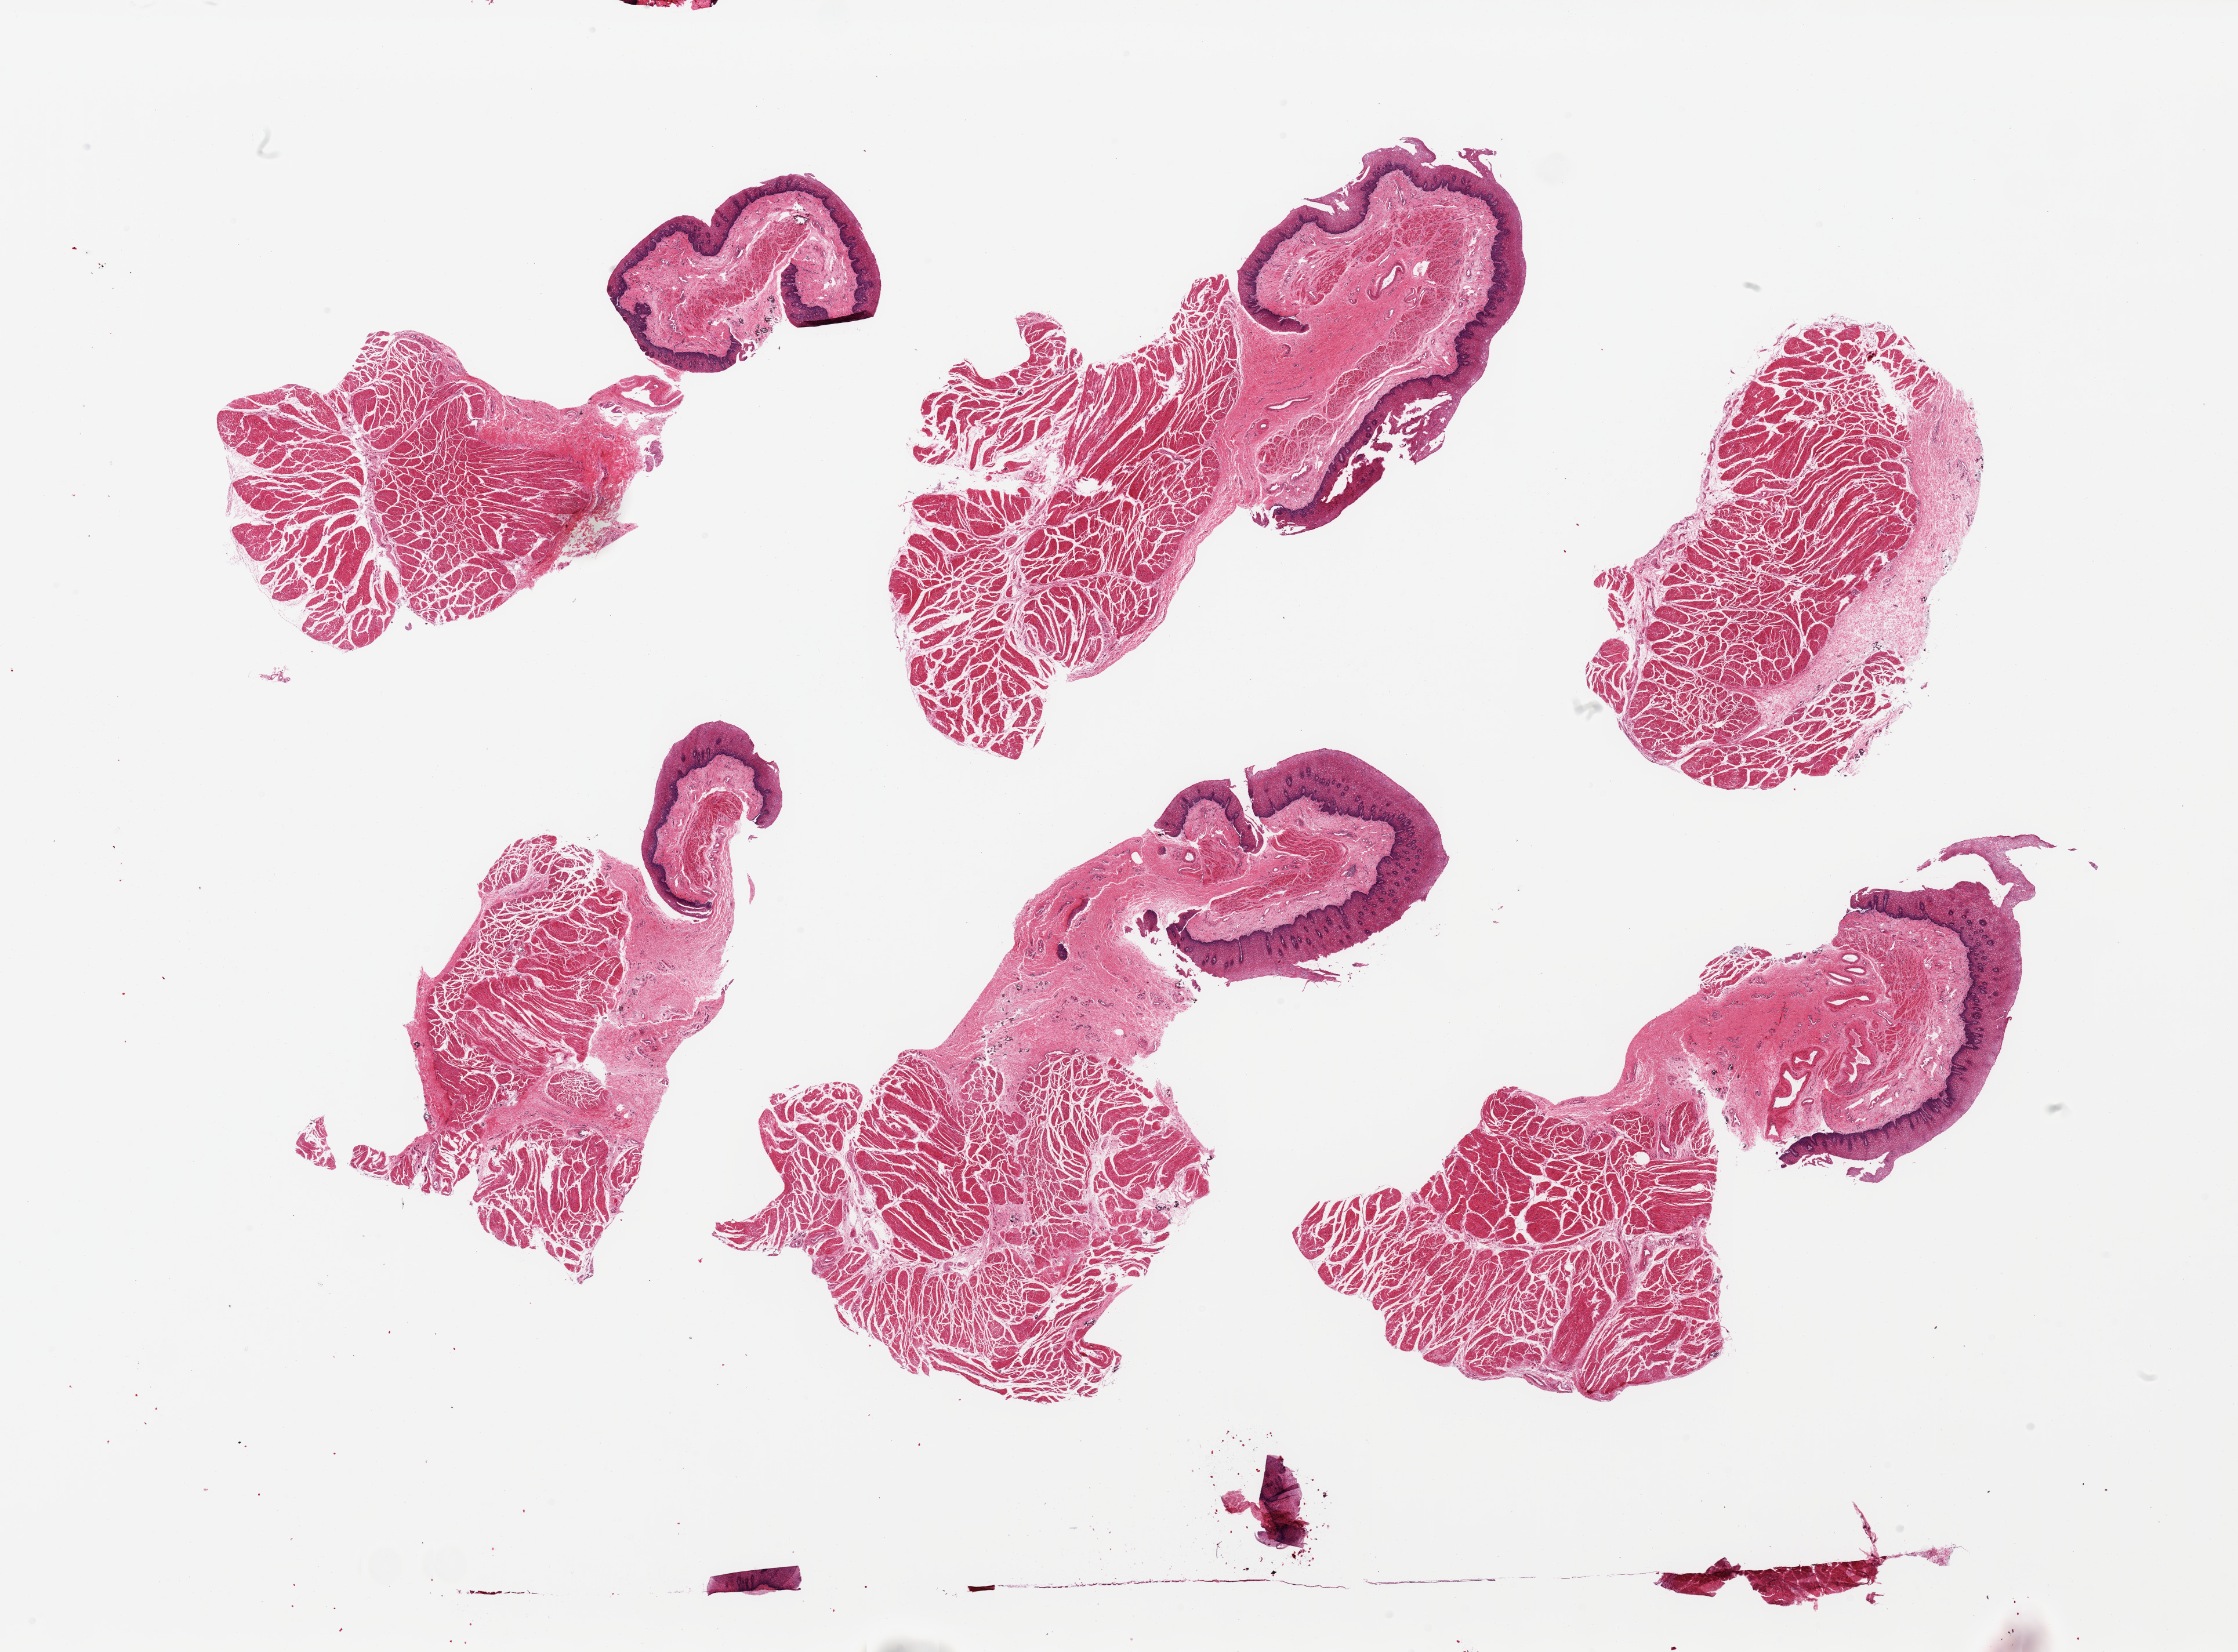
Whole-slide image, haematoxylin and eosin stain, brightfield — a low-resolution overview of the entire scanned area, about 30.5 x 22.5 mm, PAXgene-fixed paraffin-embedded (PFPE) section, target tissue: esophageal muscle, tissue donor sample.
• reviewer comment on this tissue sample: 6 pieces; non target stratified squamous epithelium with lamina propria and target muscularis